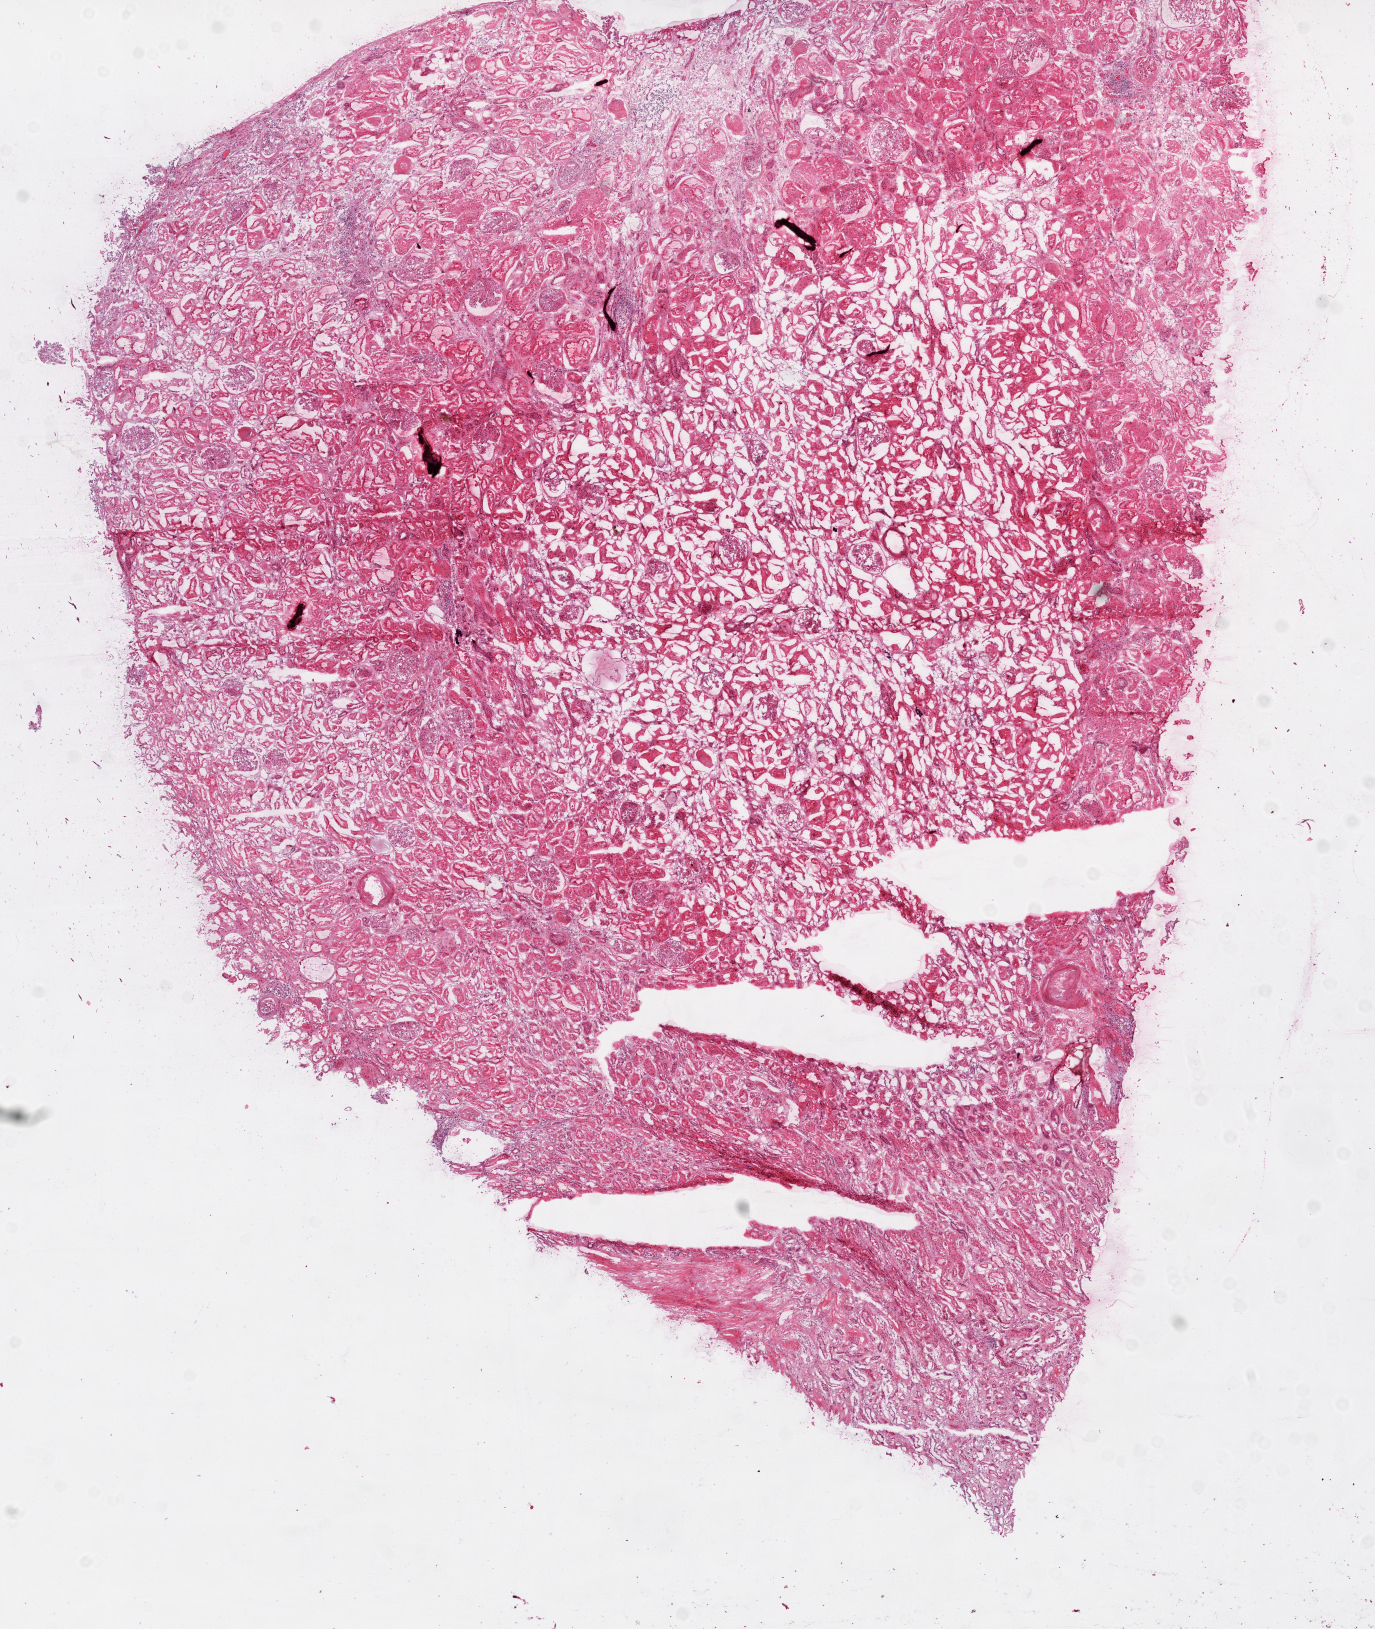
H&E whole-slide image — a low-resolution overview of the entire scanned area, about 11.0 x 13.1 mm; frozen section; kidney, solid tissue normal (non-tumour tissue) sample. Female, age 66 years at initial diagnosis.
This section: solid tissue normal sample (biorepository sample class). Patient diagnosis: Clear cell adenocarcinoma, NOS.